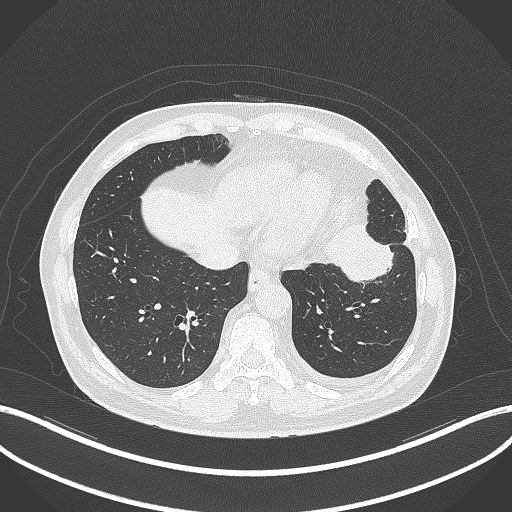
Chest CT, one axial slice. Position 98 of 230 along the scan axis. Reconstruction kernel B70f. 120 kVp. Lung window (W 1500 / L -600 HU). 1 mm slice thickness. 512 × 512 image matrix, field of view 400 × 400 mm. Male patient, age 68 years. From the clinical record (not read from this slice): clinical TNM (as recorded): T2b N0 M0.
Annotated regions visible in this slice (bounding box drawn by a radiologist):
- lung tumour (recorded histology: squamous cell carcinoma): bounding box [x1, y1, x2, y2] px = [323, 220, 396, 285]